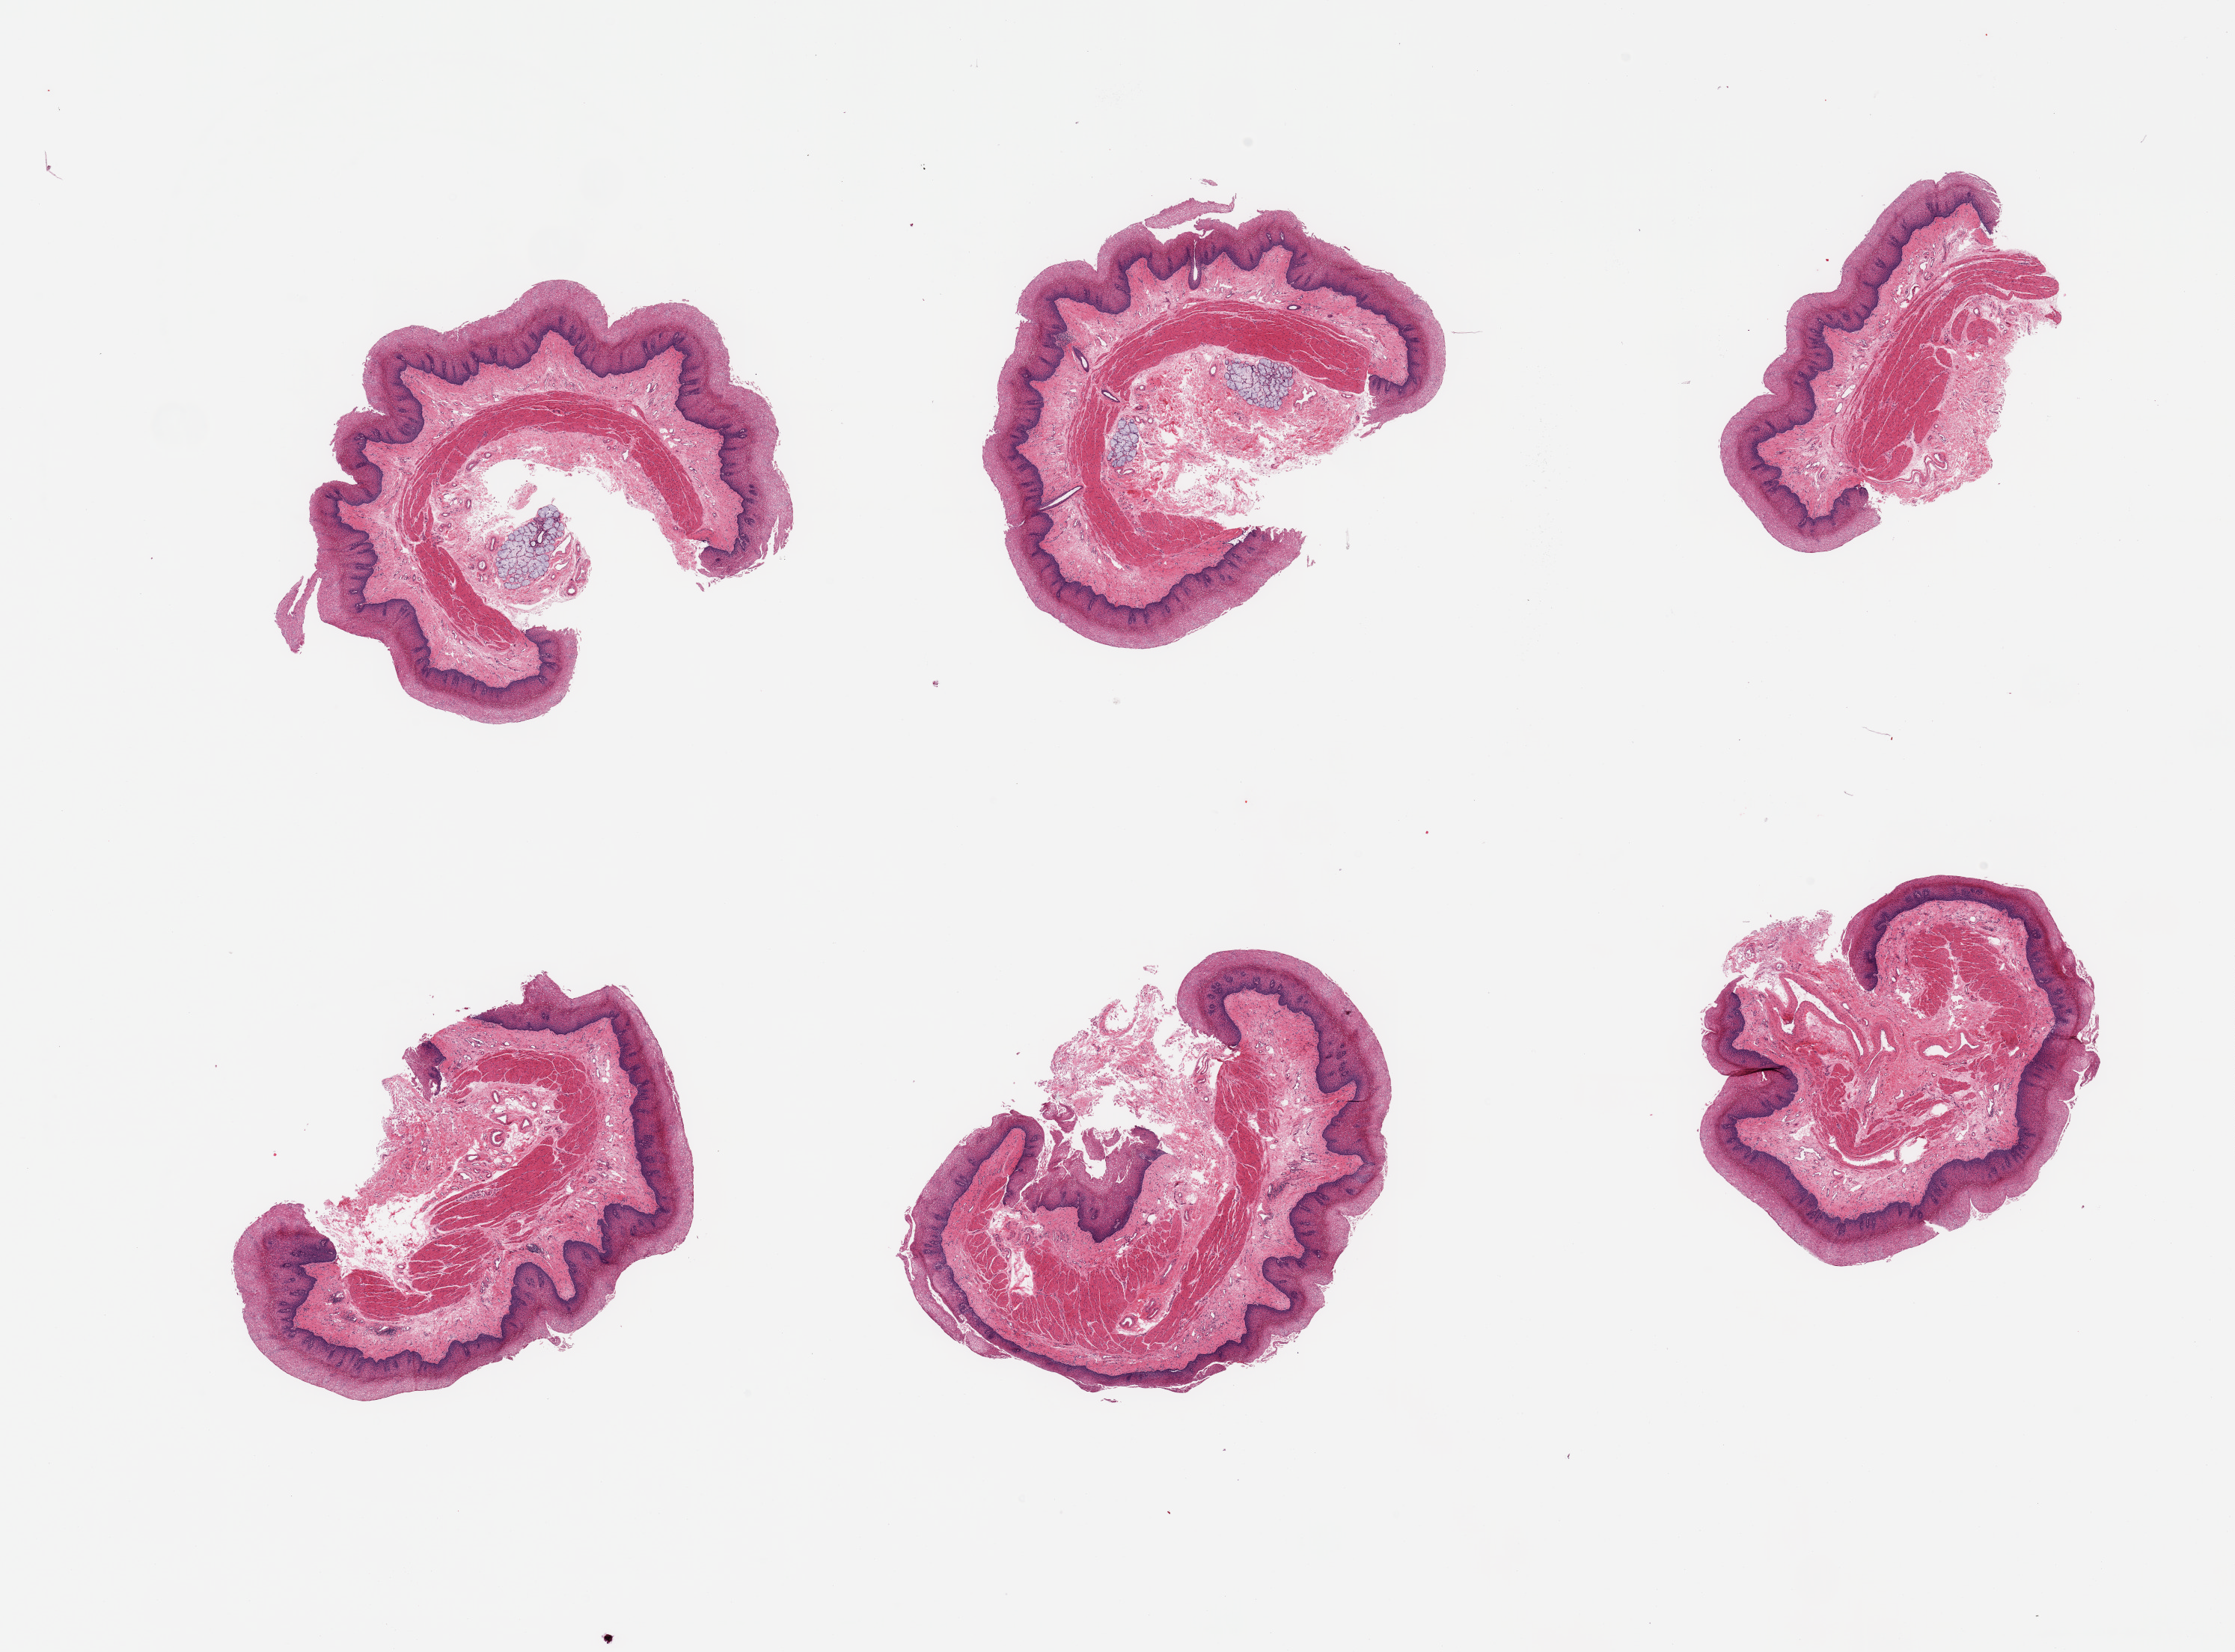
Digitized haematoxylin and eosin-stained section — shown as a low-resolution overview of the whole scanned area (about 23.6 x 17.5 mm), PAXgene-fixed paraffin-embedded (PFPE) section, sampled site (target tissue): esophageal mucous membrane, tissue donor sample. Female donor.
- pathologist's review note for this sample: 6 pieces, squamous mucosa up to ~0.7mm, few submucosal mucus glands noted